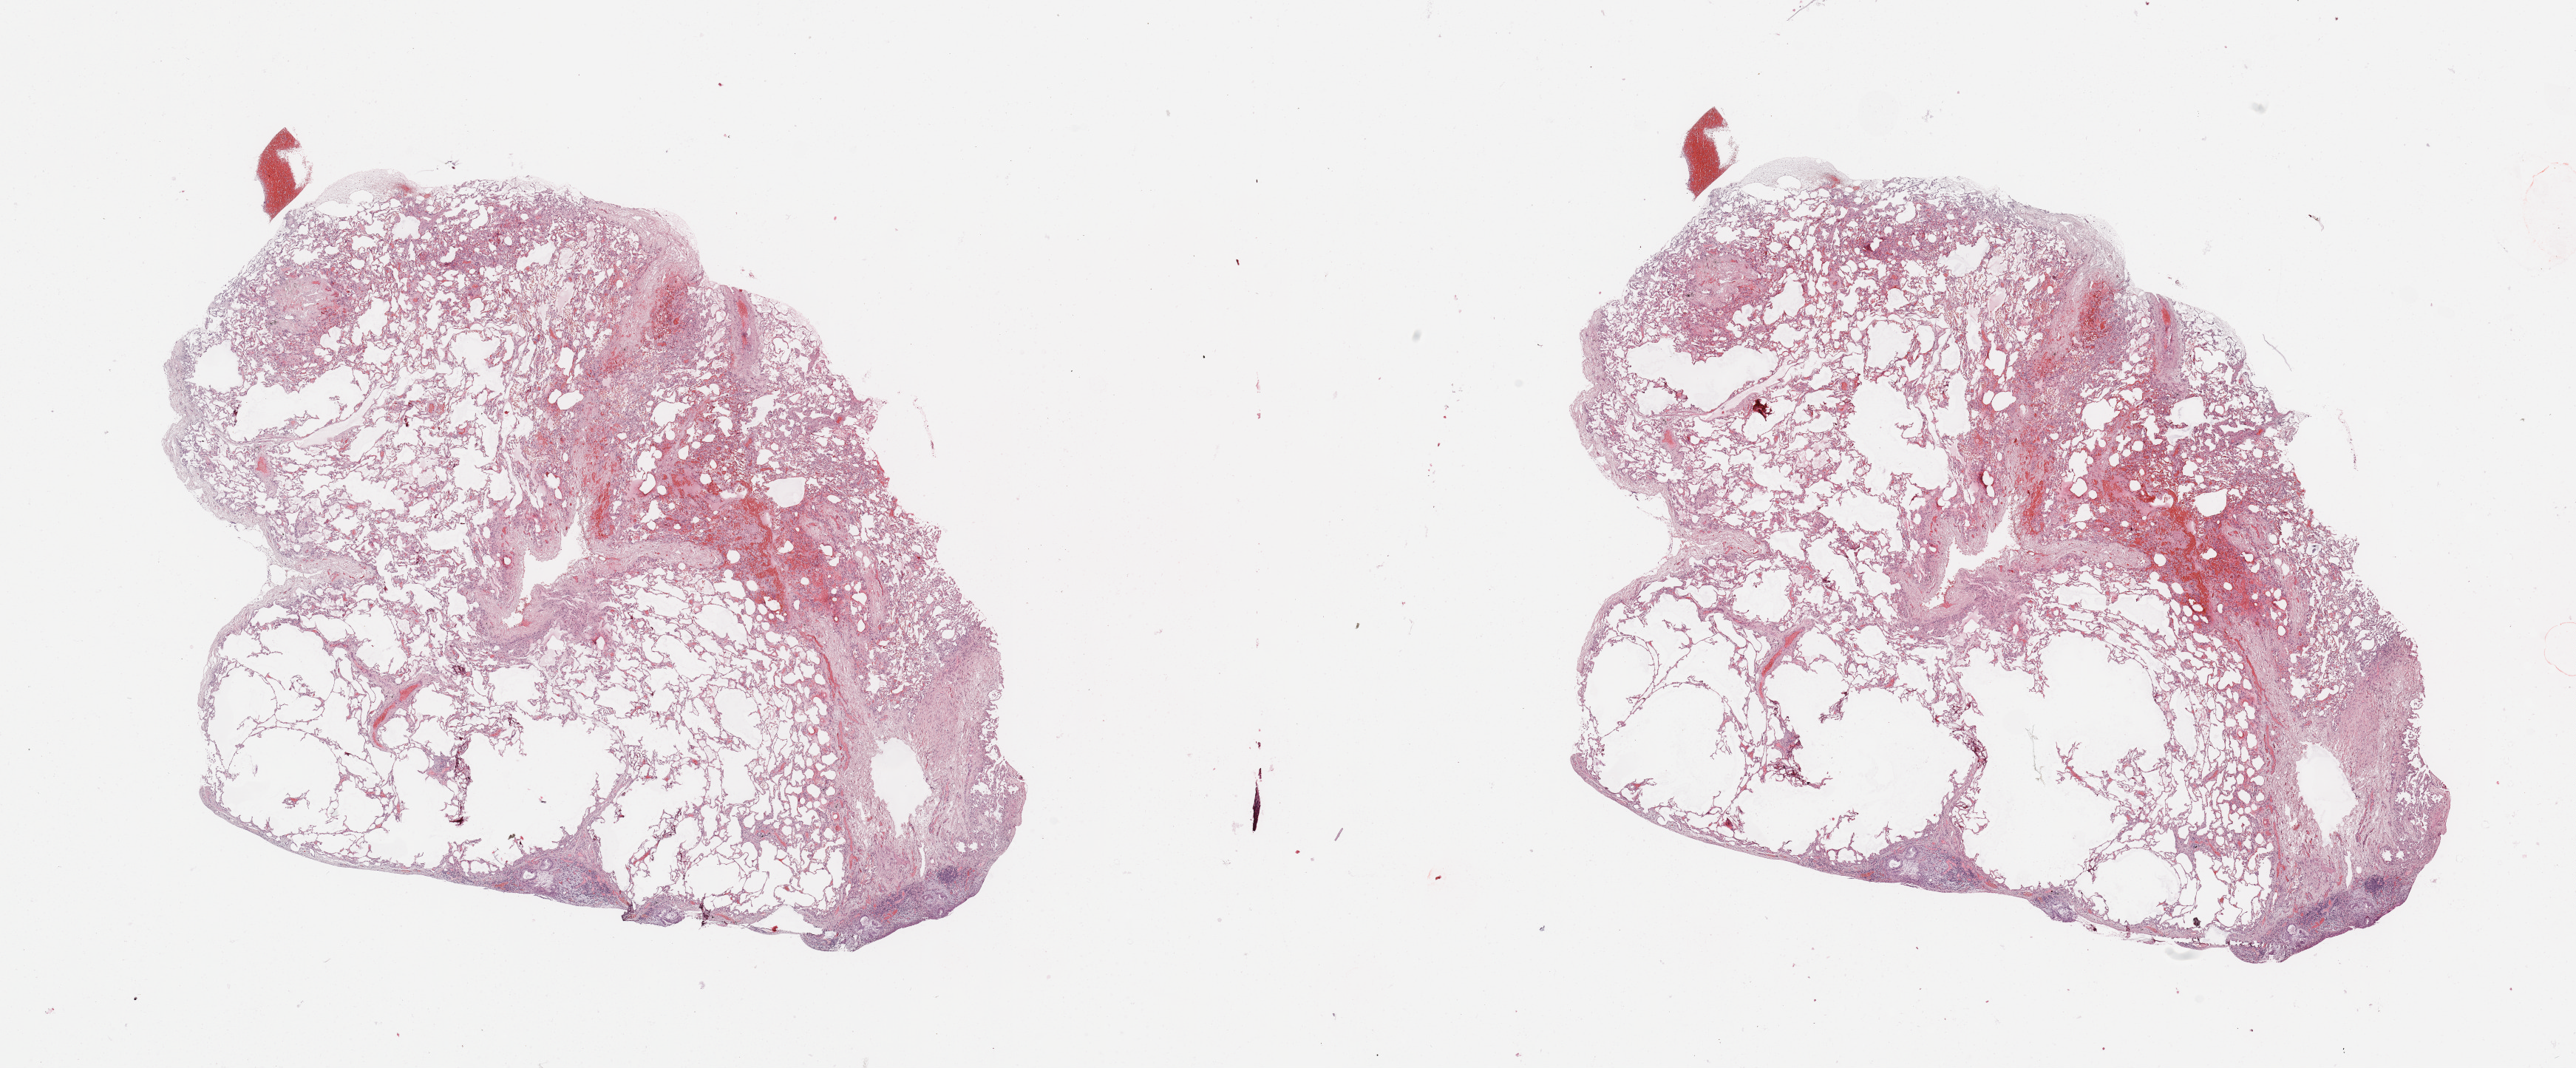
H&E whole-slide image — low-resolution overview of the scanned area, about 27.6 x 11.4 mm (slide scanned at 20x), lung, tissue type not recorded.
Patient diagnosis (cohort enrolment): lung adenocarcinoma (lung).